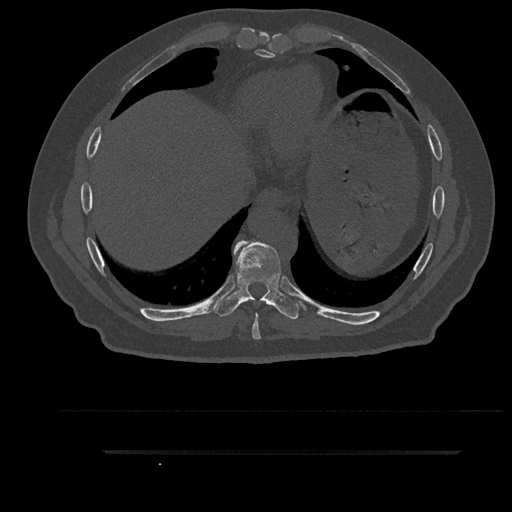
CT including the spine, one axial slice. Slice 439 of 797 in the series (ordered by position). Reconstruction kernel Br40s/3. Bone window (W 1800 / L 400 HU). 0.5 mm slice thickness. 512 × 512 image matrix, field of view 432 × 432 mm. Patient: male, 63 years. Case-level facts recorded for this patient, not image findings: primary cancer: renal; vertebrae with lytic lesions (as recorded): T8.
Outlined on this slice (semi-automatic segmentation, software-assisted and operator-edited):
- T8 vertebra: bounding box <252,305,274,340> (left, top, right, bottom; pixels)
- T9 vertebra: <213,240,300,319>